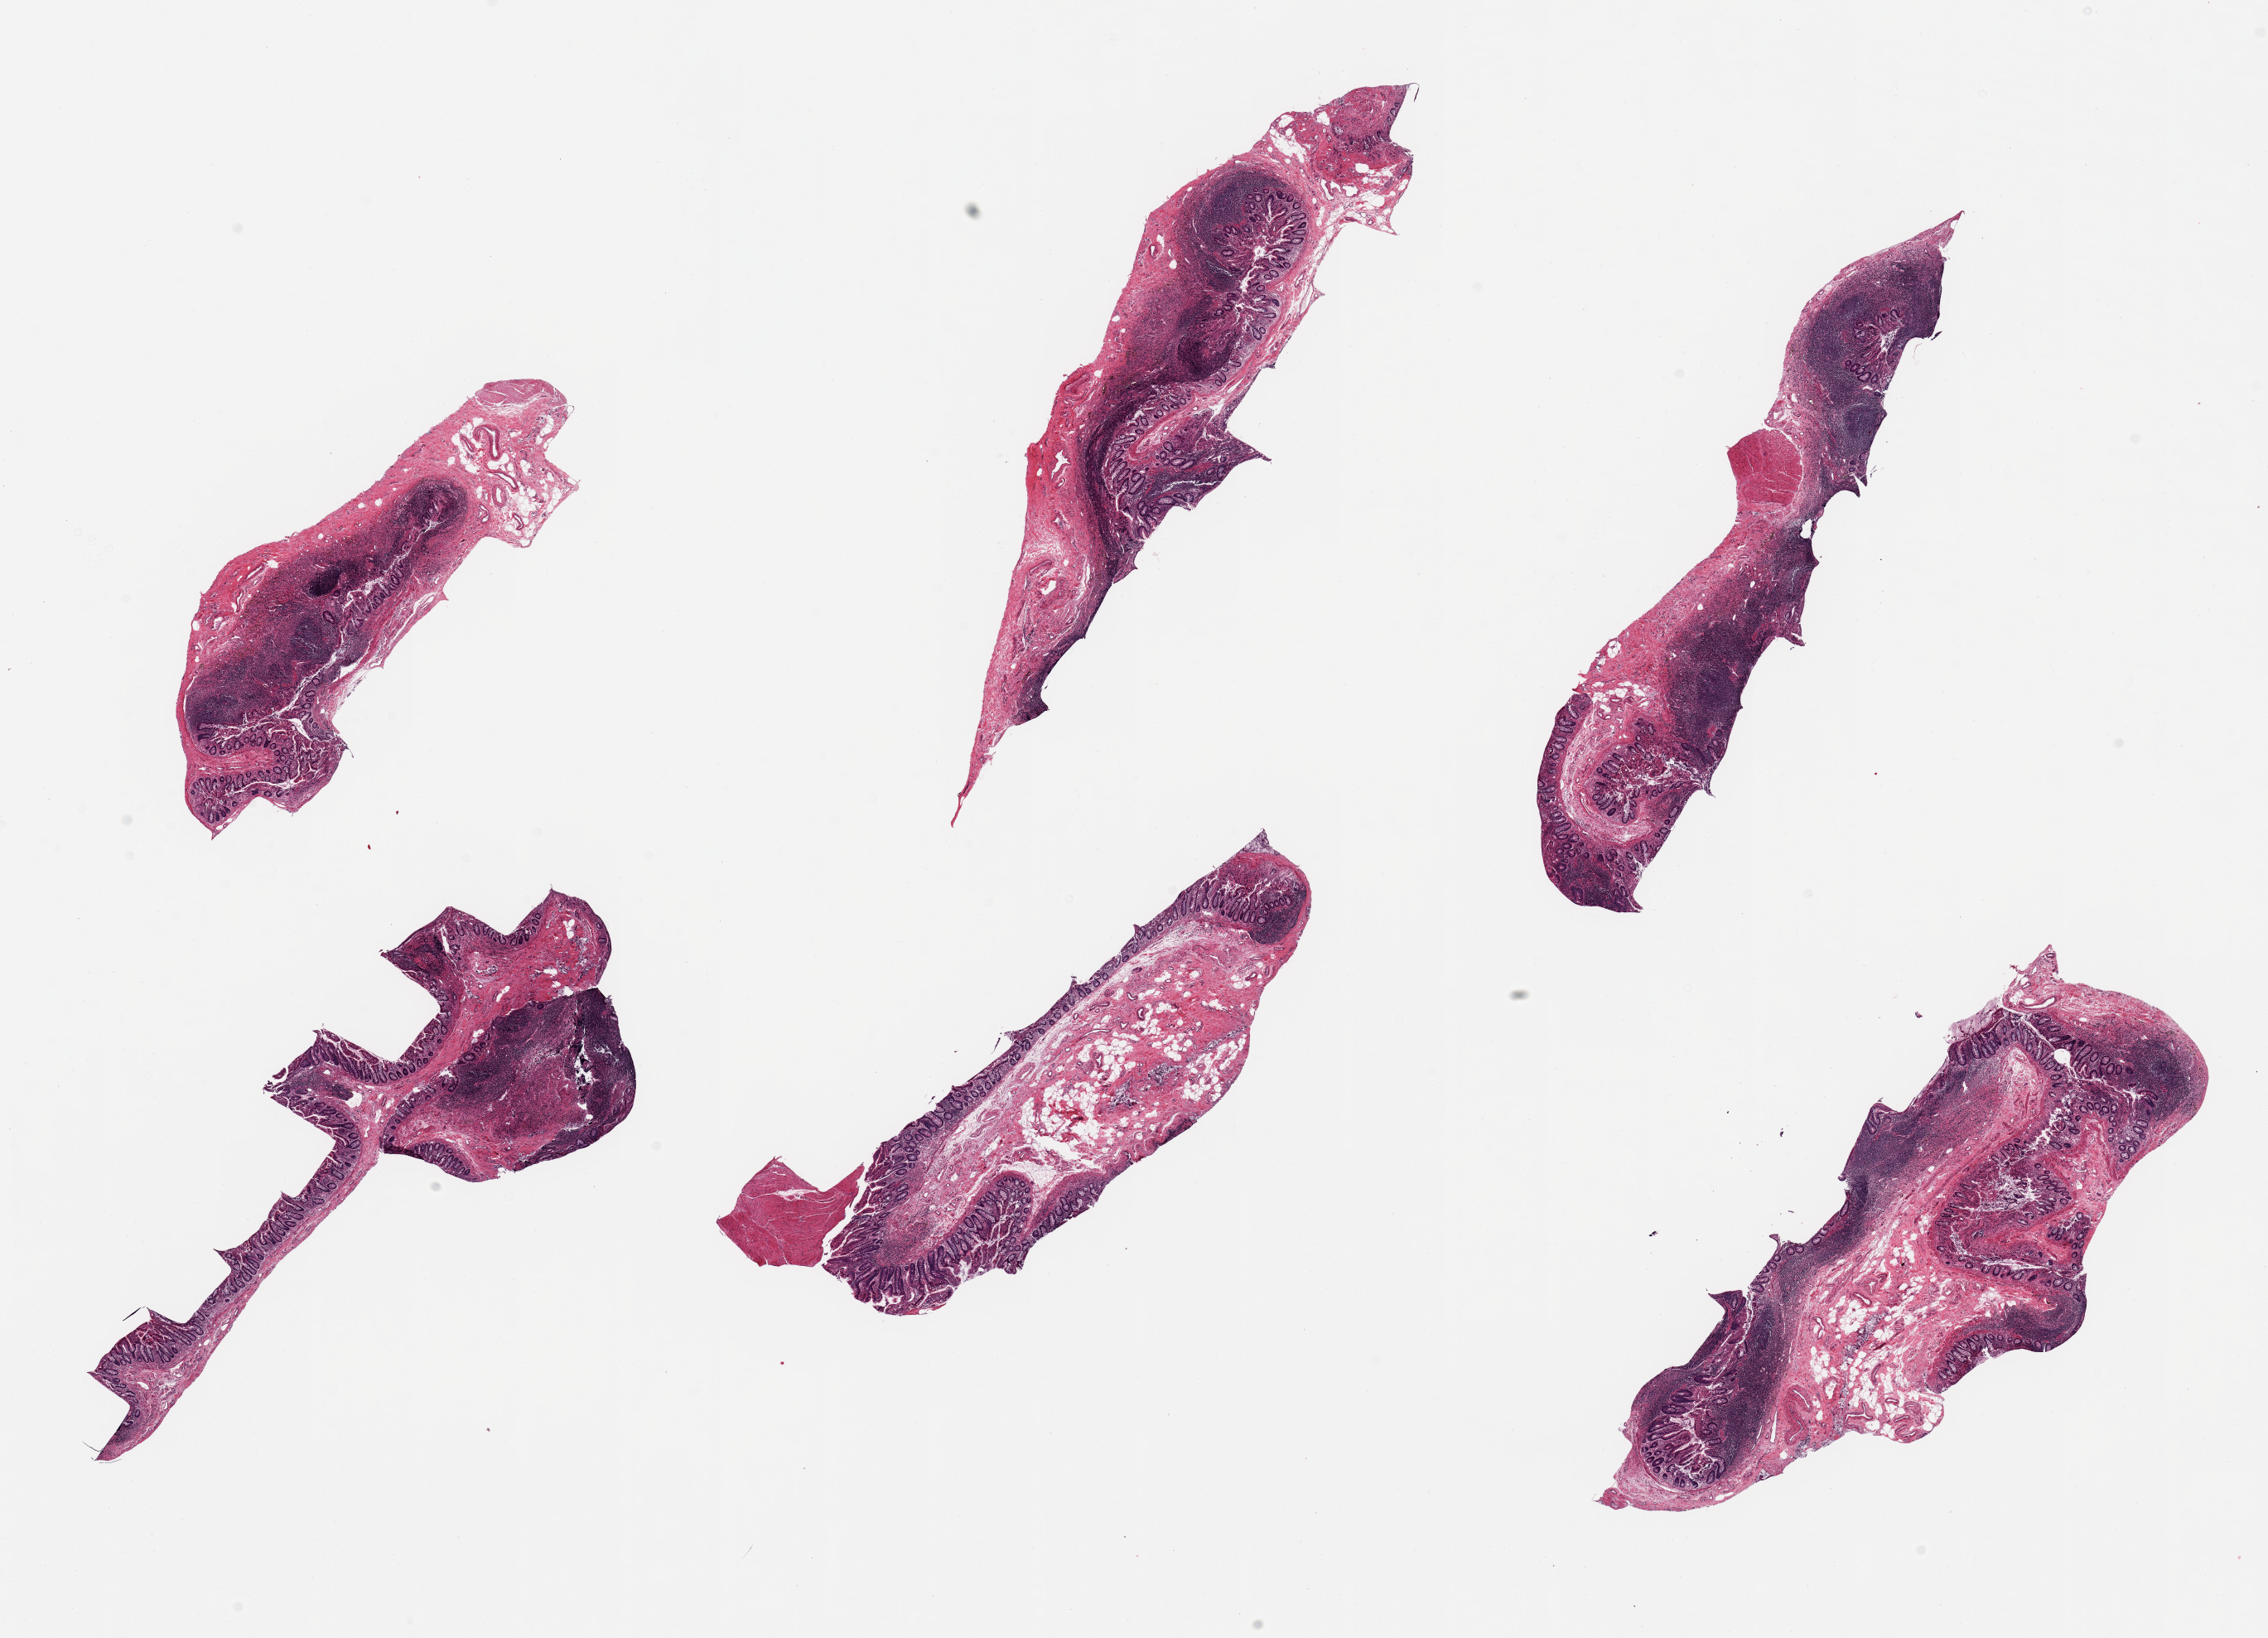
Whole-slide image, hematoxylin and eosin (H&E) stain — shown as a low-resolution overview of the whole scanned area (about 21.7 x 15.6 mm); PAXgene-fixed, paraffin-embedded tissue; section of ileum (target tissue); tissue donor sample.
Pathologist's review note for this sample: 6 pieces; mucosa and abundant target mucosal lymphoid tissue, few foci of muscularis.